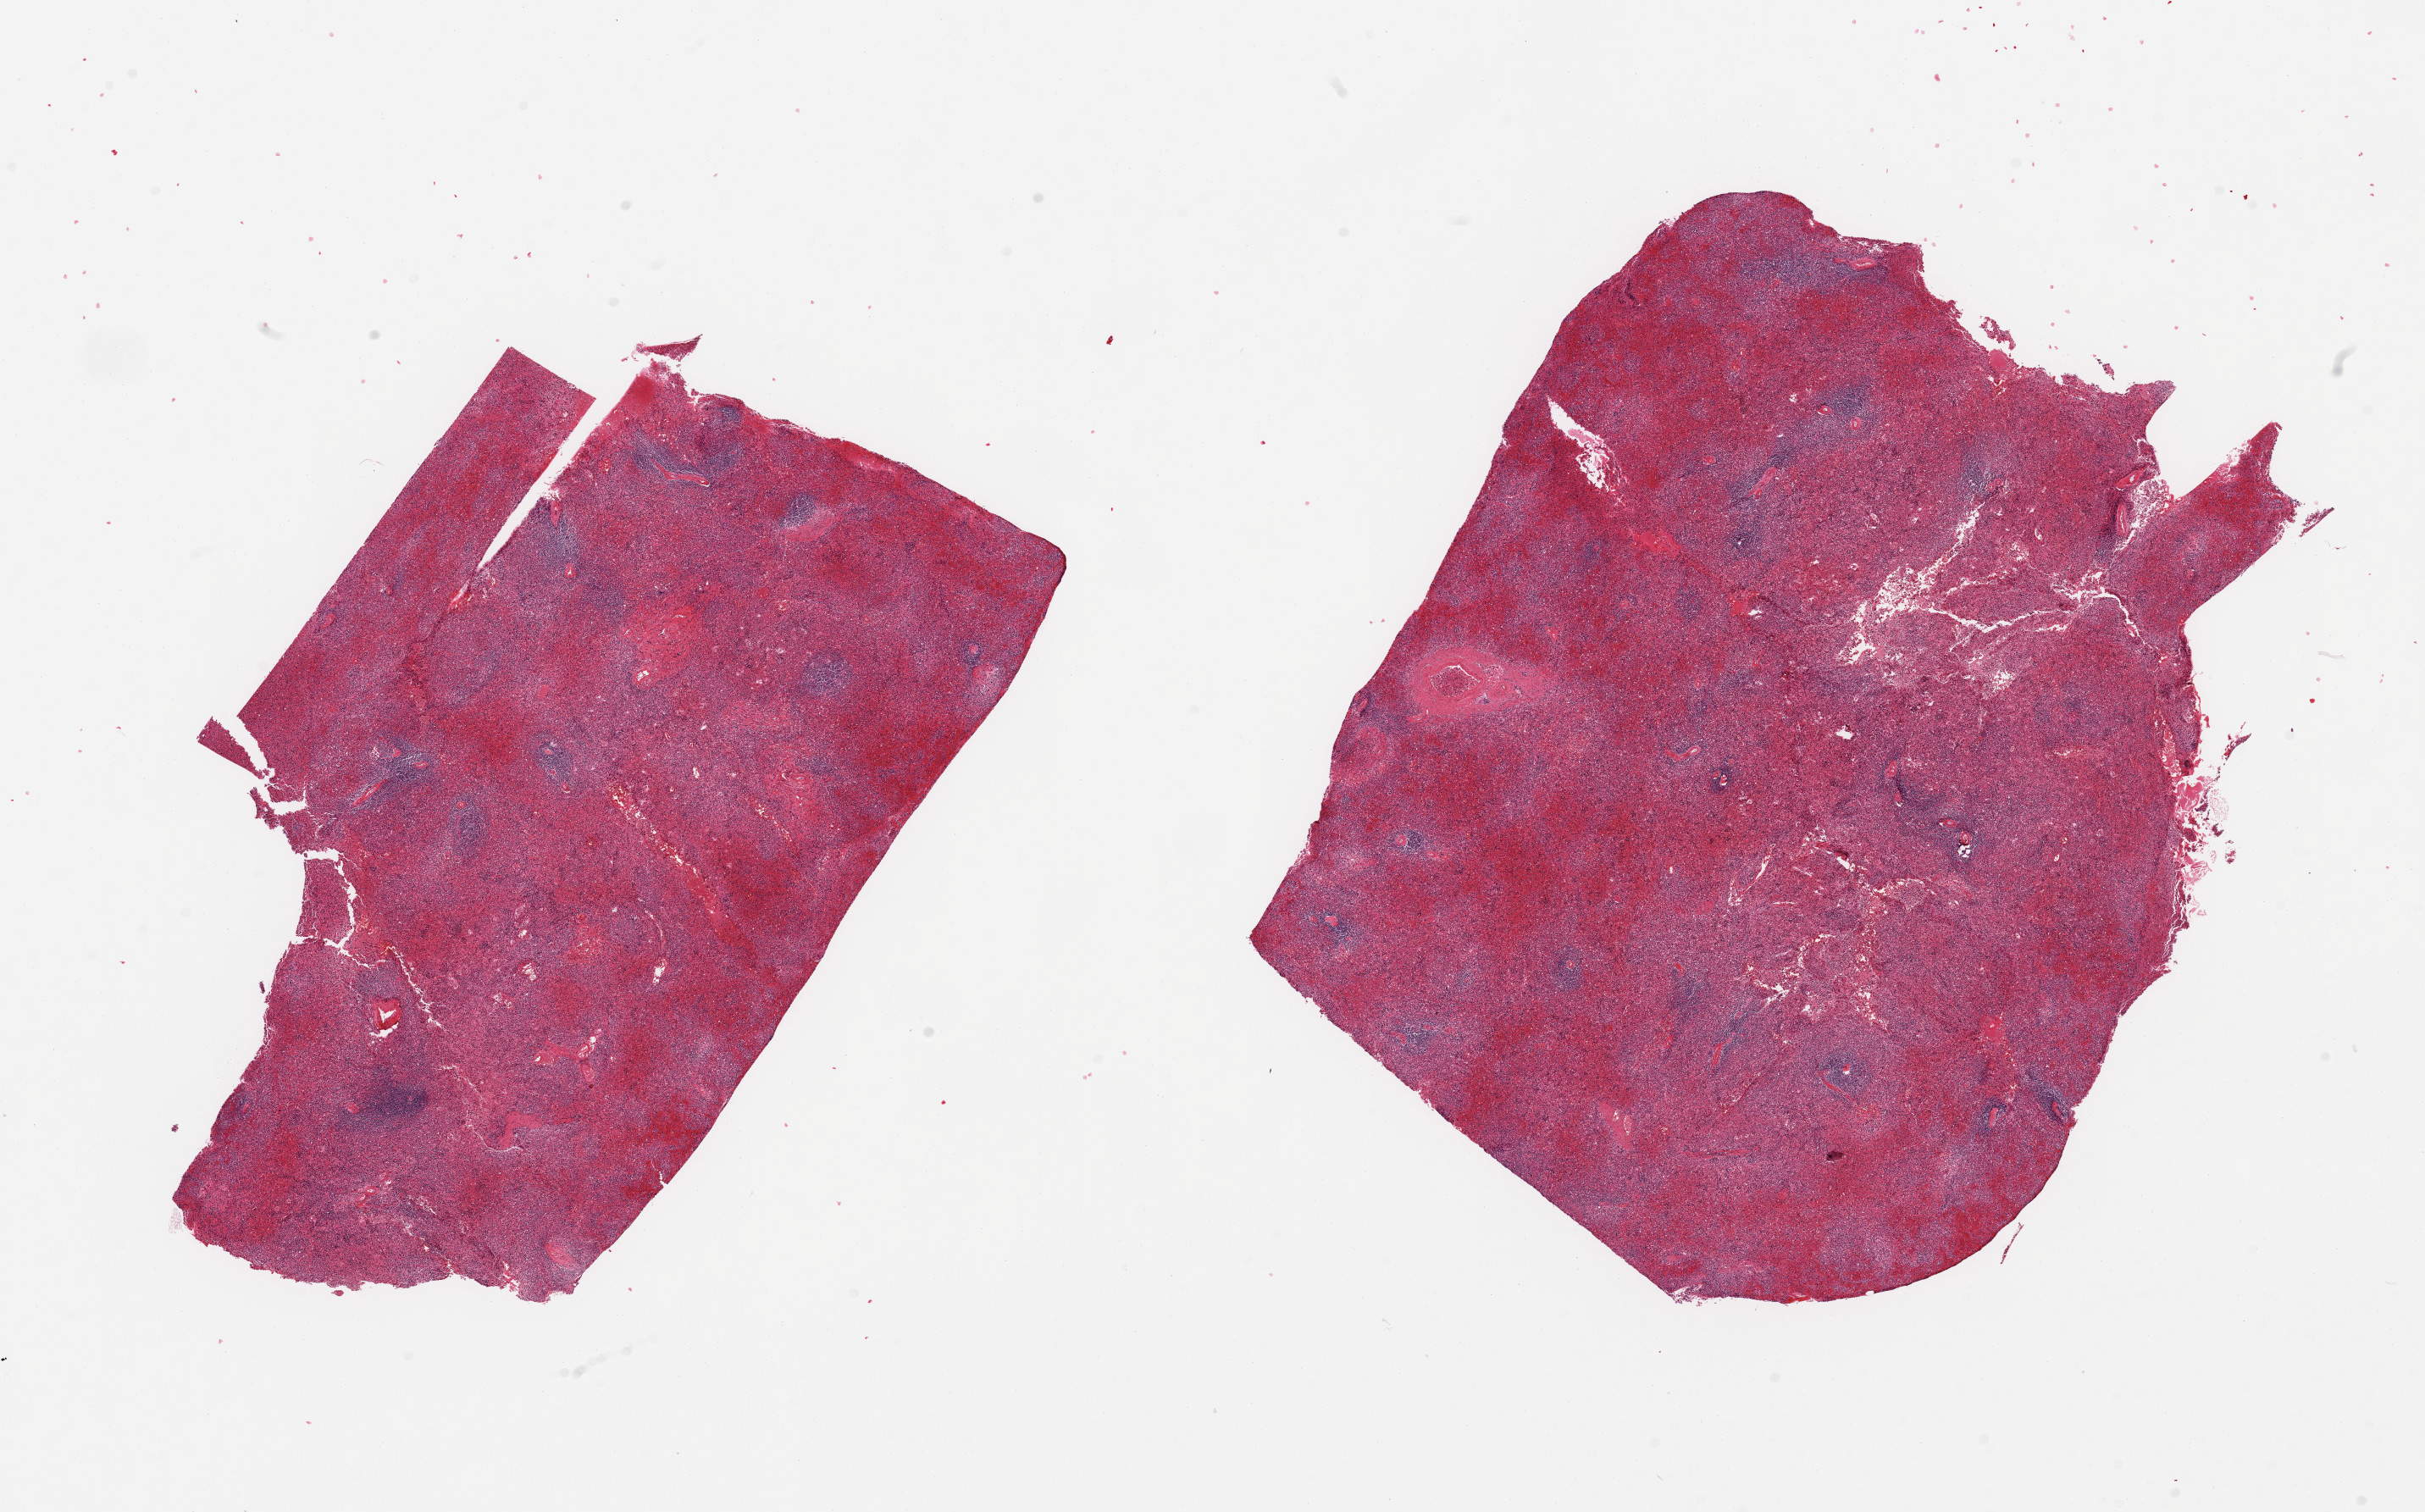
Whole-slide image, H&E stain — a low-resolution overview of the entire scanned area, about 22.6 x 14.1 mm. PAXgene-fixed paraffin-embedded (PFPE) section. Target tissue: spleen. Donor tissue sample.
Pathologist's review note for this sample: 2 pieces, marked congestion and autolysis.